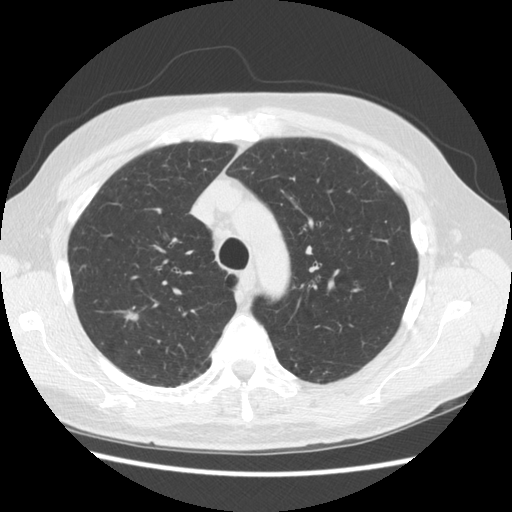
Low-dose screening chest CT, one axial slice; position 116 of 156 along the scan axis; reconstruction kernel STANDARD; 140 kVp; lung window (W 1500 / L -600 HU); 512 × 512 image matrix, field of view 360 × 360 mm.
Structures marked on this image (manually delineated by an expert):
- lesion 1 (tumor, upper lobe of right lung): bounding box <125,310,140,322> (left, top, right, bottom; pixels)